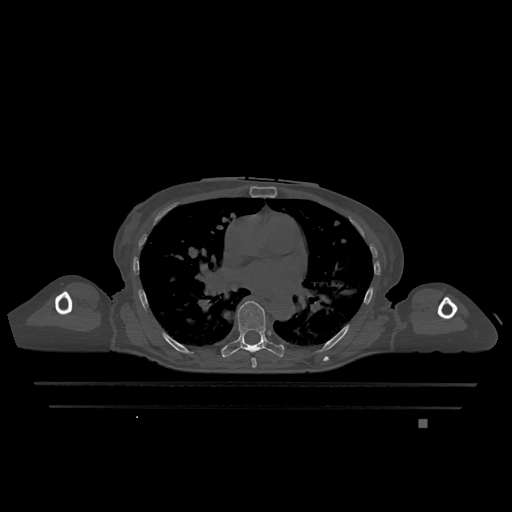
CT including the spine, one axial slice. Slice 746 of 1317 in the series (ordered by position). Bone window (W 1800 / L 400 HU). 0.5 mm slice thickness. 512 × 512 image matrix, field of view 500 × 500 mm. Female patient, age 74 years. From the clinical record (not read from this slice): primary cancer: lung.
Outlined on this slice (semi-automatic segmentation, software-assisted and operator-edited):
- T6 vertebra: bounding box (x1, y1, x2, y2) in pixels: (251, 357, 257, 368)
- T7 vertebra: (221, 301, 285, 358)